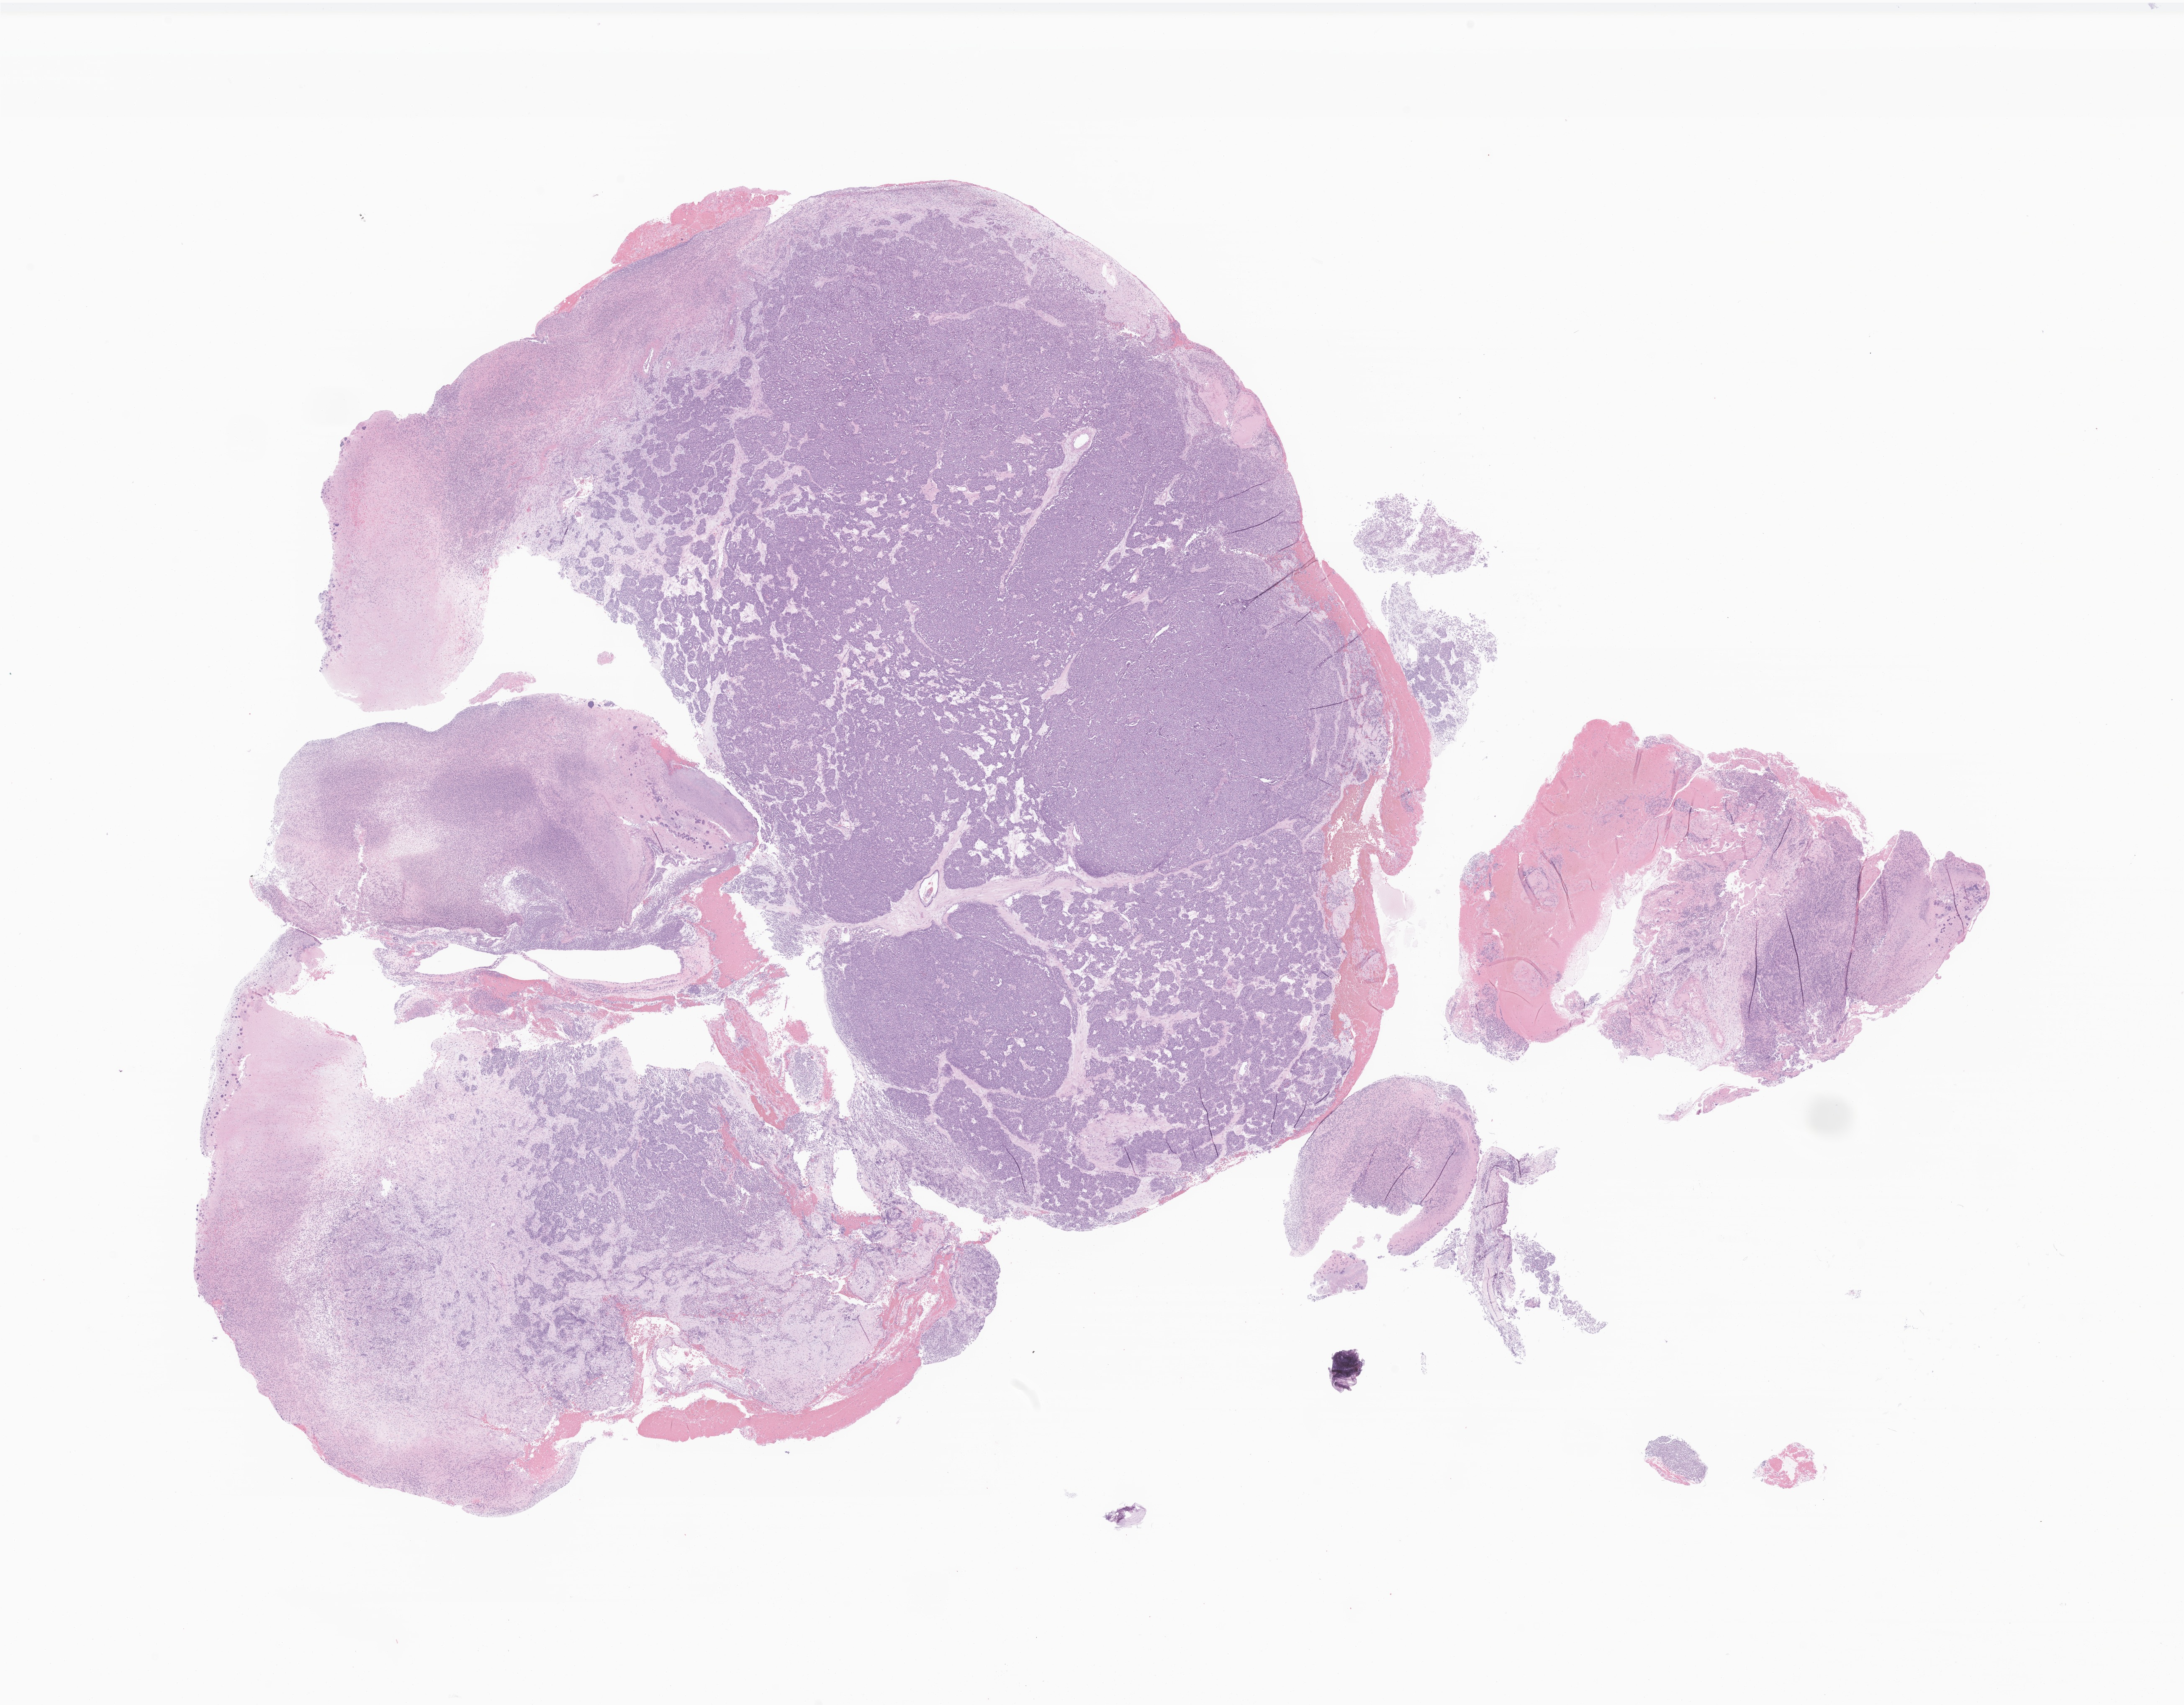
Digitized hematoxylin and eosin (H&E)-stained section of tumor tissue from the lung, low-resolution overview of the scanned area, about 22.0 x 17.2 mm. Formalin-fixed, paraffin-embedded (FFPE) tissue. Male patient, age 181 months.
Diagnosis: Neuroendocrine carcinoma, NOS.